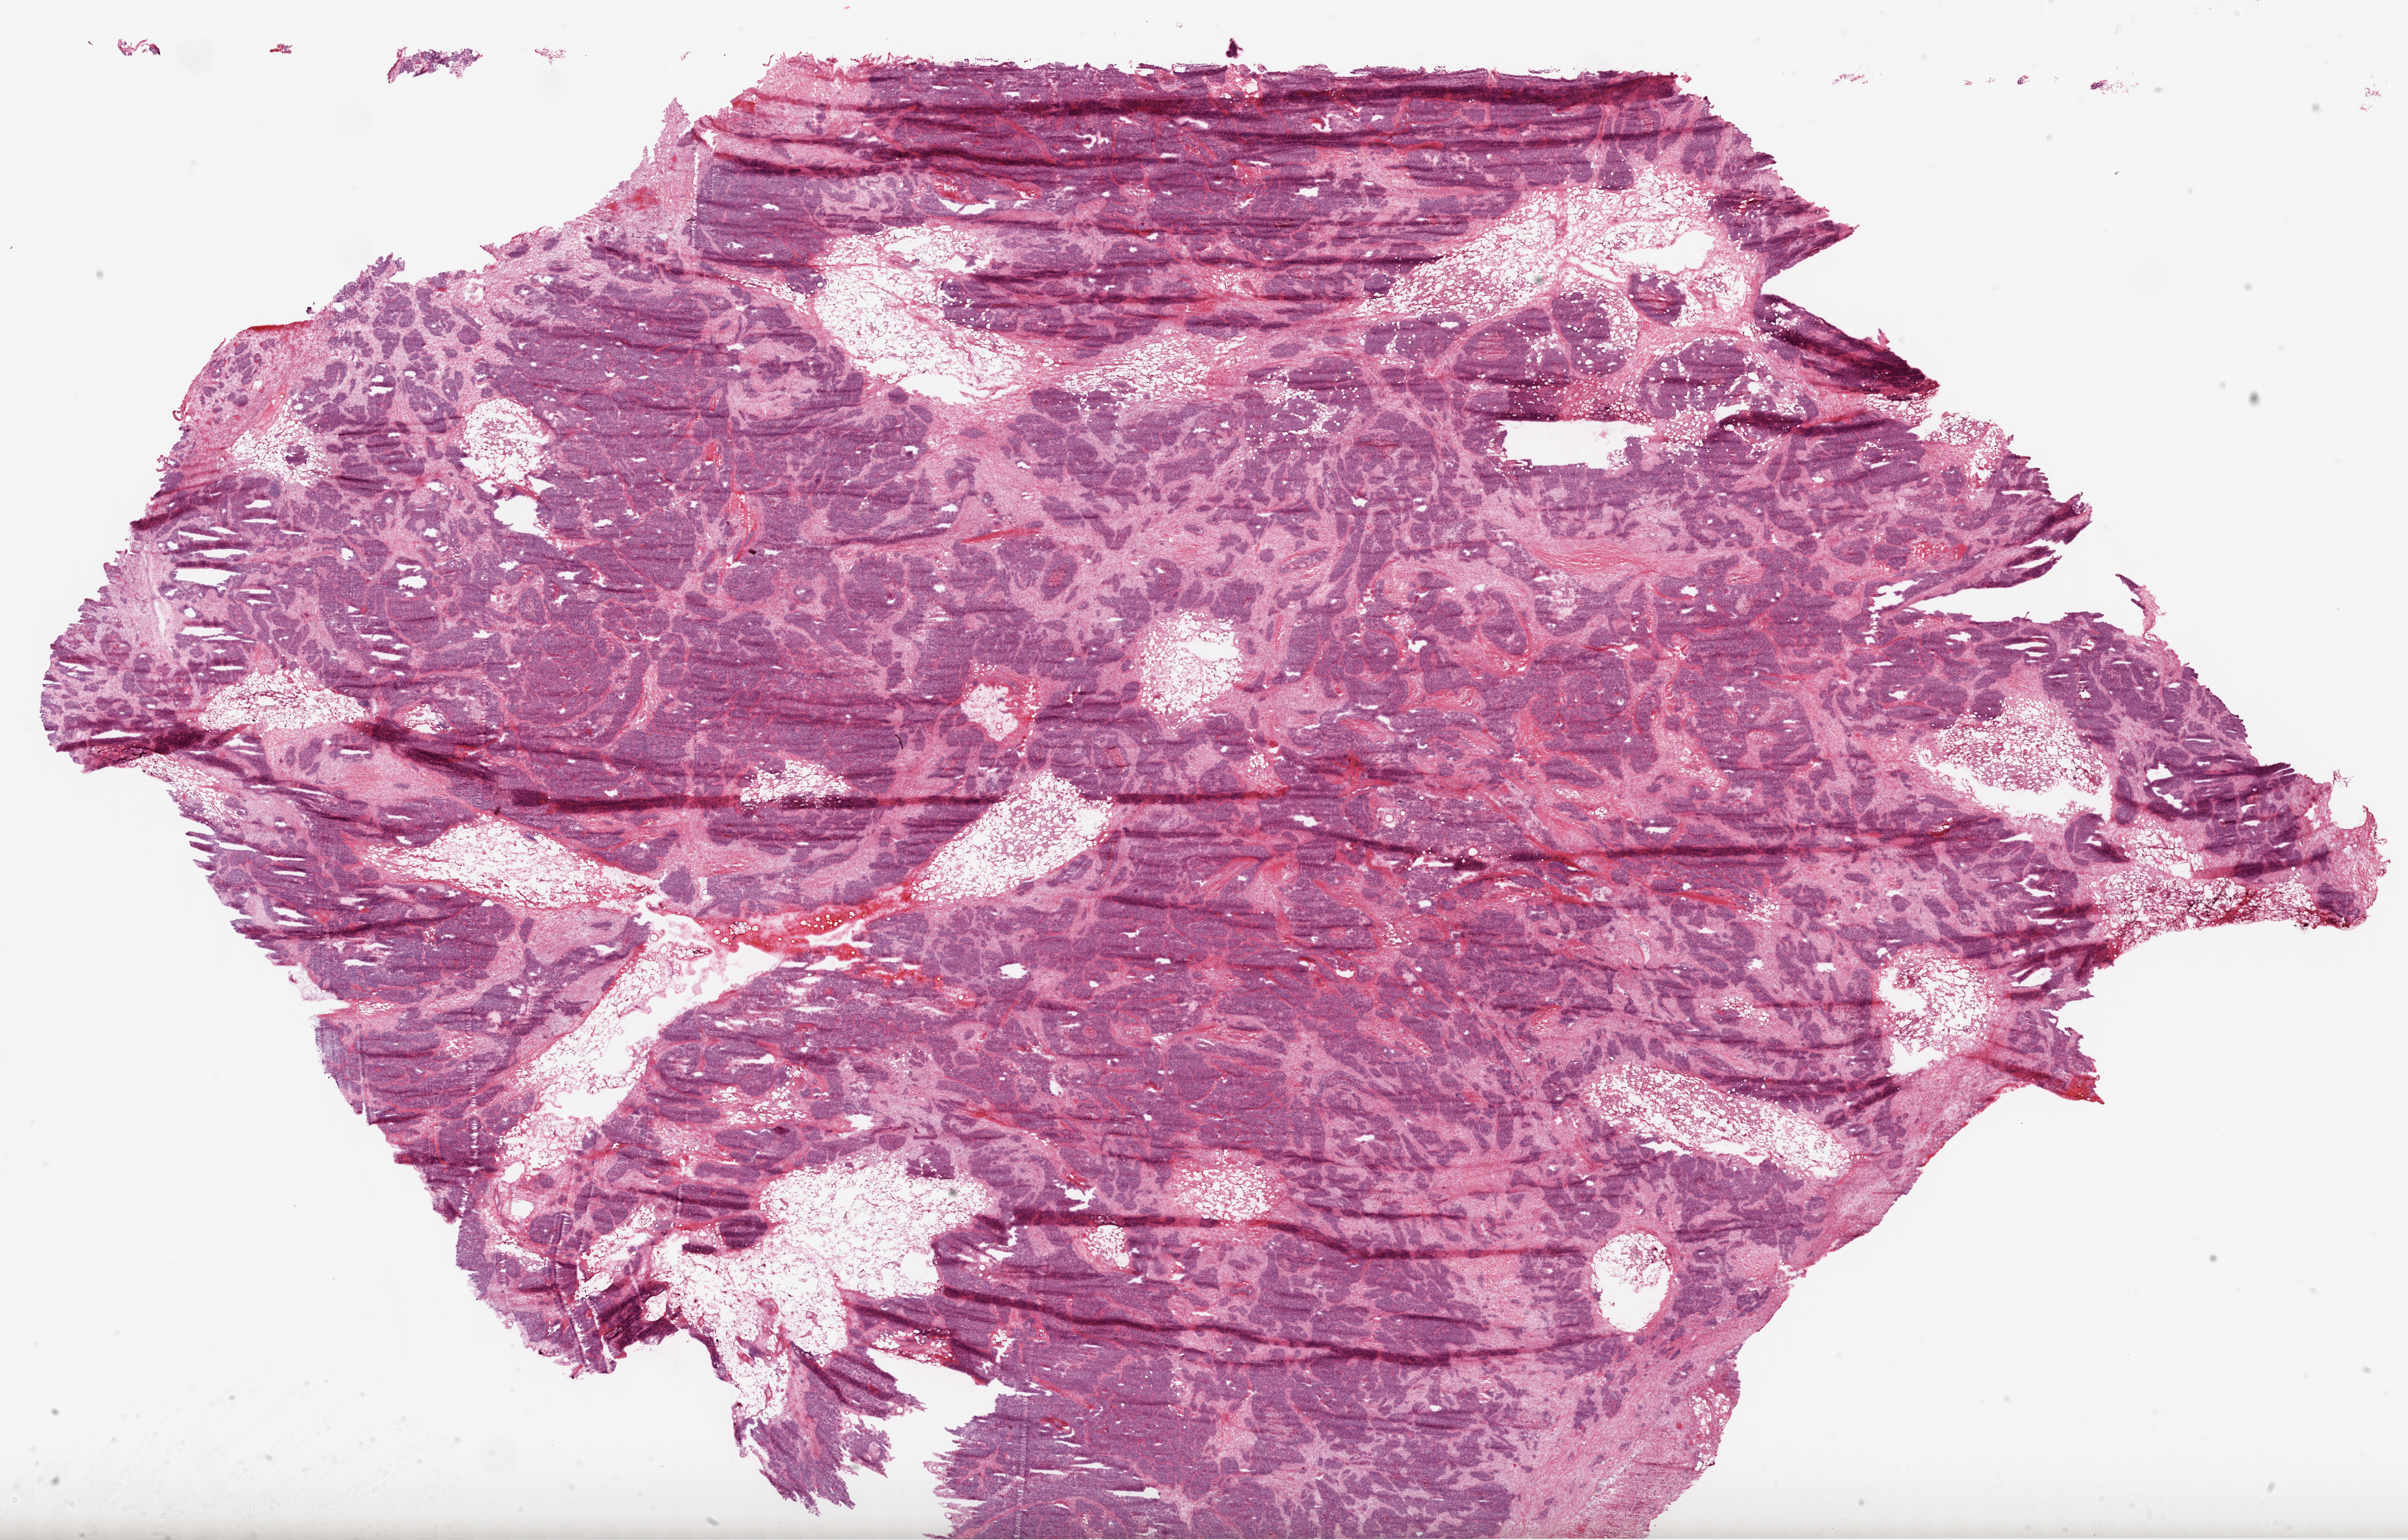
Whole-slide histology image, H&E — a low-resolution overview of the entire scanned area, about 31.9 x 20.4 mm (from a 20x scan). Frozen section from the top of the tissue portion. Primary tumour sample from the ovary. Female, age 76 years at initial diagnosis. Histologic grade: G3 (poorly differentiated). Pathologist review of this section (percent, as recorded): tumour cells 75%, tumour nuclei 95%, normal cells 0%, stromal cells 5%, necrosis 10%.
Histologic diagnosis: Serous cystadenocarcinoma, NOS. Laterality: bilateral. FIGO stage: IIIC.